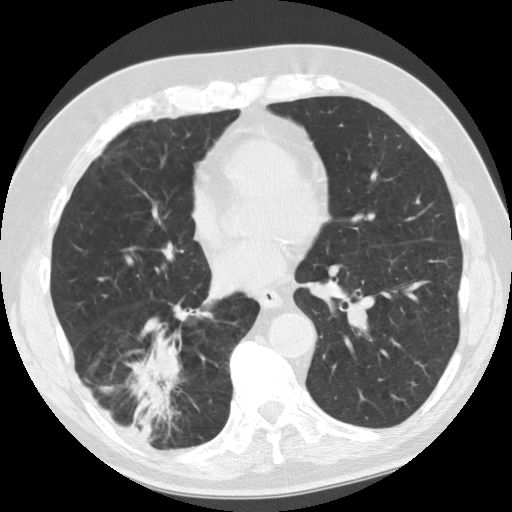
Low-dose screening chest CT, one axial slice. Slice 52 of 135 in the series (ordered by position). Lung window (W 1500 / L -600 HU). 2.5 mm slice thickness. 512 × 512 image matrix.
Structures marked on this image (manually delineated by an expert):
- lesion 1 (tumor, lower lobe of right lung): box from (x=128, y=333) to (x=181, y=440) px